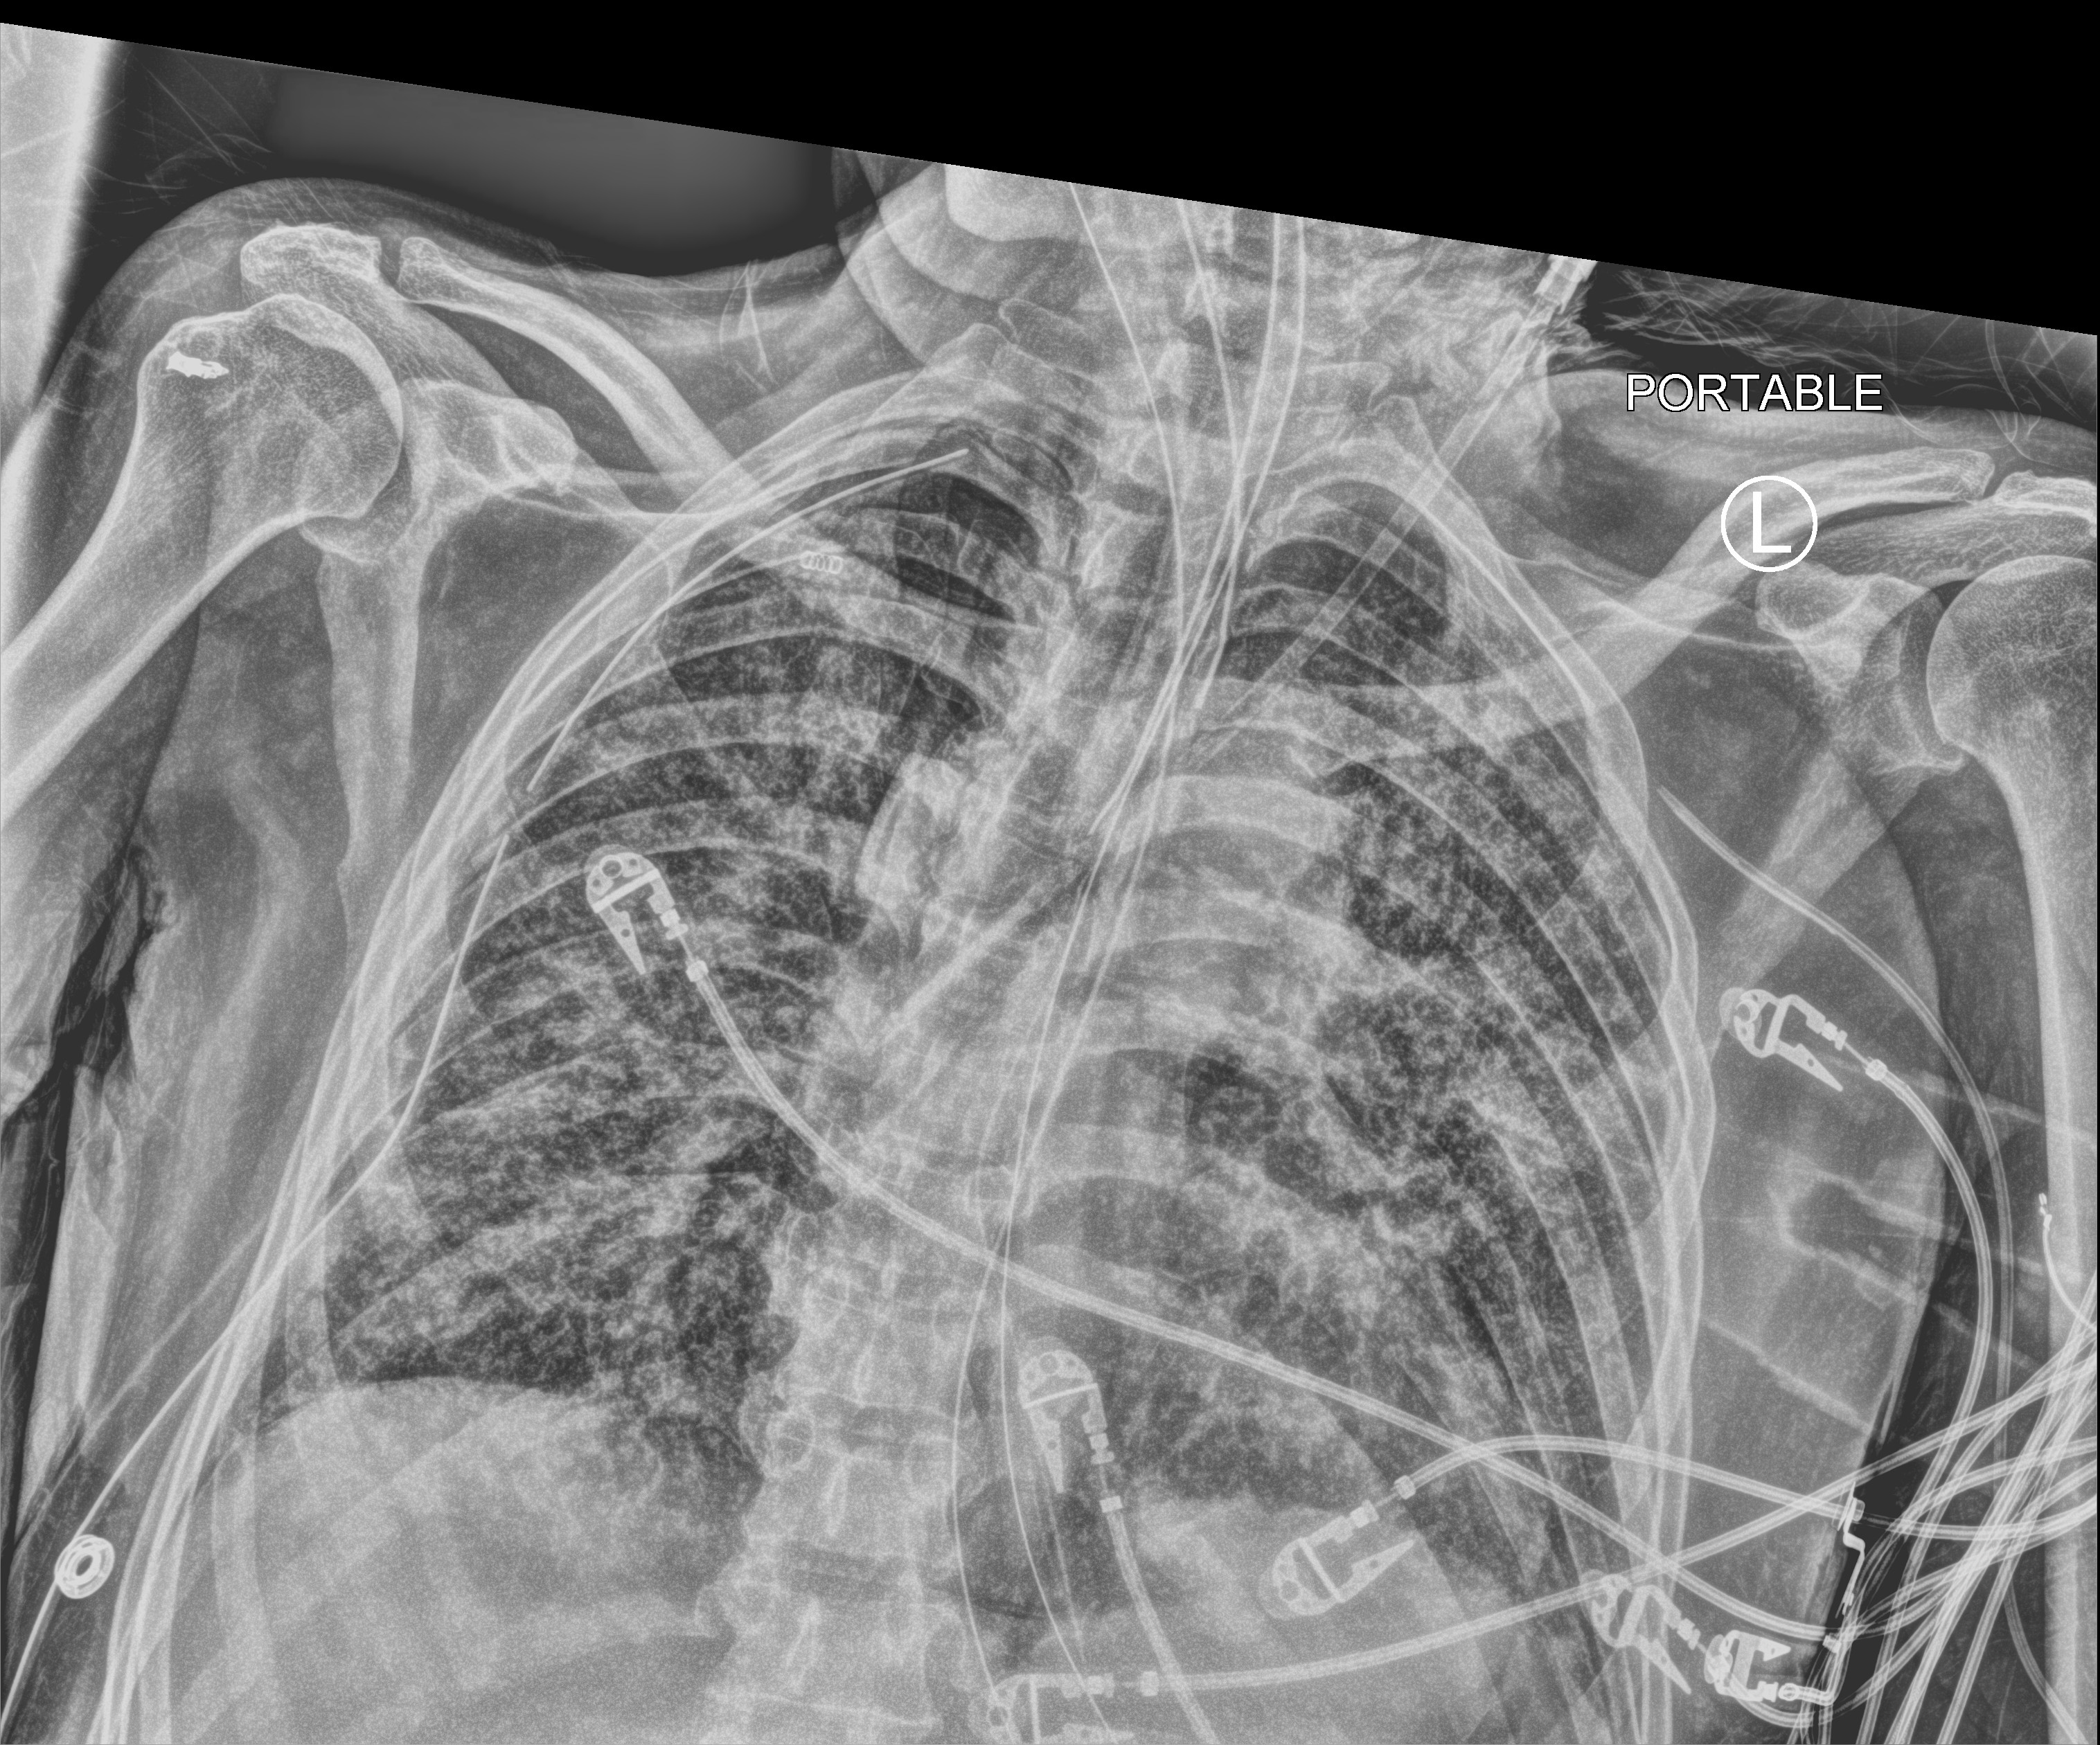
Bedside chest radiograph (computed radiography); anteroposterior (AP) projection. Patient hospitalised with COVID-19; male, aged 60–74 years.
From the hospital-stay record, not from the radiograph (when in the stay this image was taken is not recorded): mechanically ventilated during this hospital stay: yes; chronic kidney disease (admission record): no; admitted to intensive care during this hospital stay: yes.